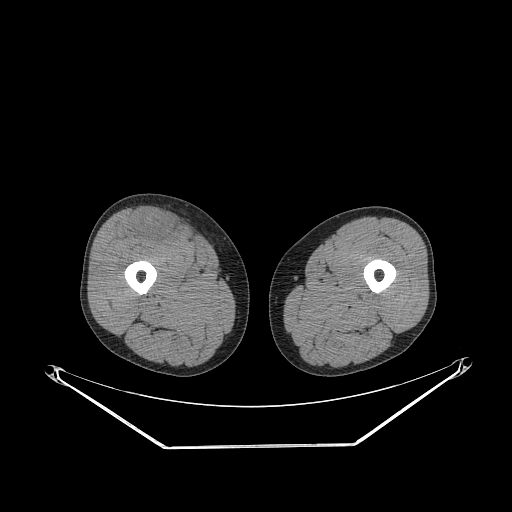
CT of an extremity soft-tissue mass (from a PET/CT study), one axial slice; slice 259 of 311 in the series (ordered by position); soft-tissue window (W 400 / L 40 HU); 512 × 512 image matrix, field of view 500 × 500 mm. Male patient. From the clinical record (not read from this slice): histological type: pleiomorphic leiomyosarcoma; grade: intermediate; site of the primary tumour: right thigh.
Outlined on this slice (expert contour drawn on MRI and transferred to this co-registered scan by the dataset authors):
- gross tumour volume including surrounding oedema: box from (x=133, y=210) to (x=179, y=241) px